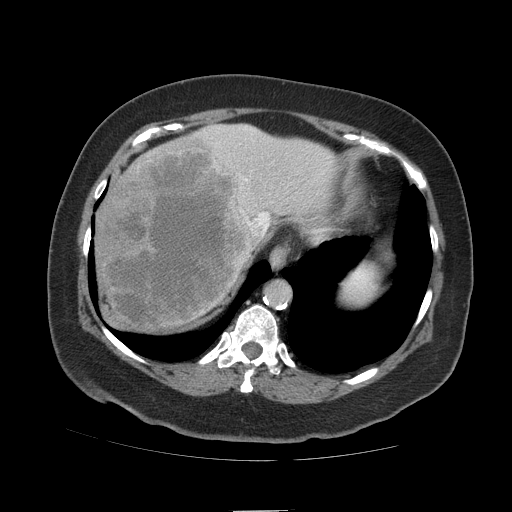
Contrast-enhanced abdominal CT (liver protocol), one axial slice. Slice 88 of 109 in the series (ordered by position). Soft-tissue window (W 400 / L 40 HU). 2.5 mm slice thickness. 512 × 512 image matrix, field of view 420 × 420 mm. Case-level facts recorded for this patient, not image findings: diagnosis: hepatocellular carcinoma (patient treated with transarterial chemoembolisation; whether this scan precedes or follows treatment is not stated here); TNM stage (as recorded): Stage-IVB; Child-Pugh class: A.
Annotated regions visible in this slice (semi-automatically segmented with operator editing):
- abdominal aorta: bounding box (x1, y1, x2, y2) in pixels: (266, 282, 290, 306)
- liver parenchyma outside the tumour (the mass and vessels are separate outlines, so this box may not span the whole liver): (94, 124, 334, 330)
- mass: (95, 136, 257, 330)
- liver vessels: (204, 126, 330, 236)